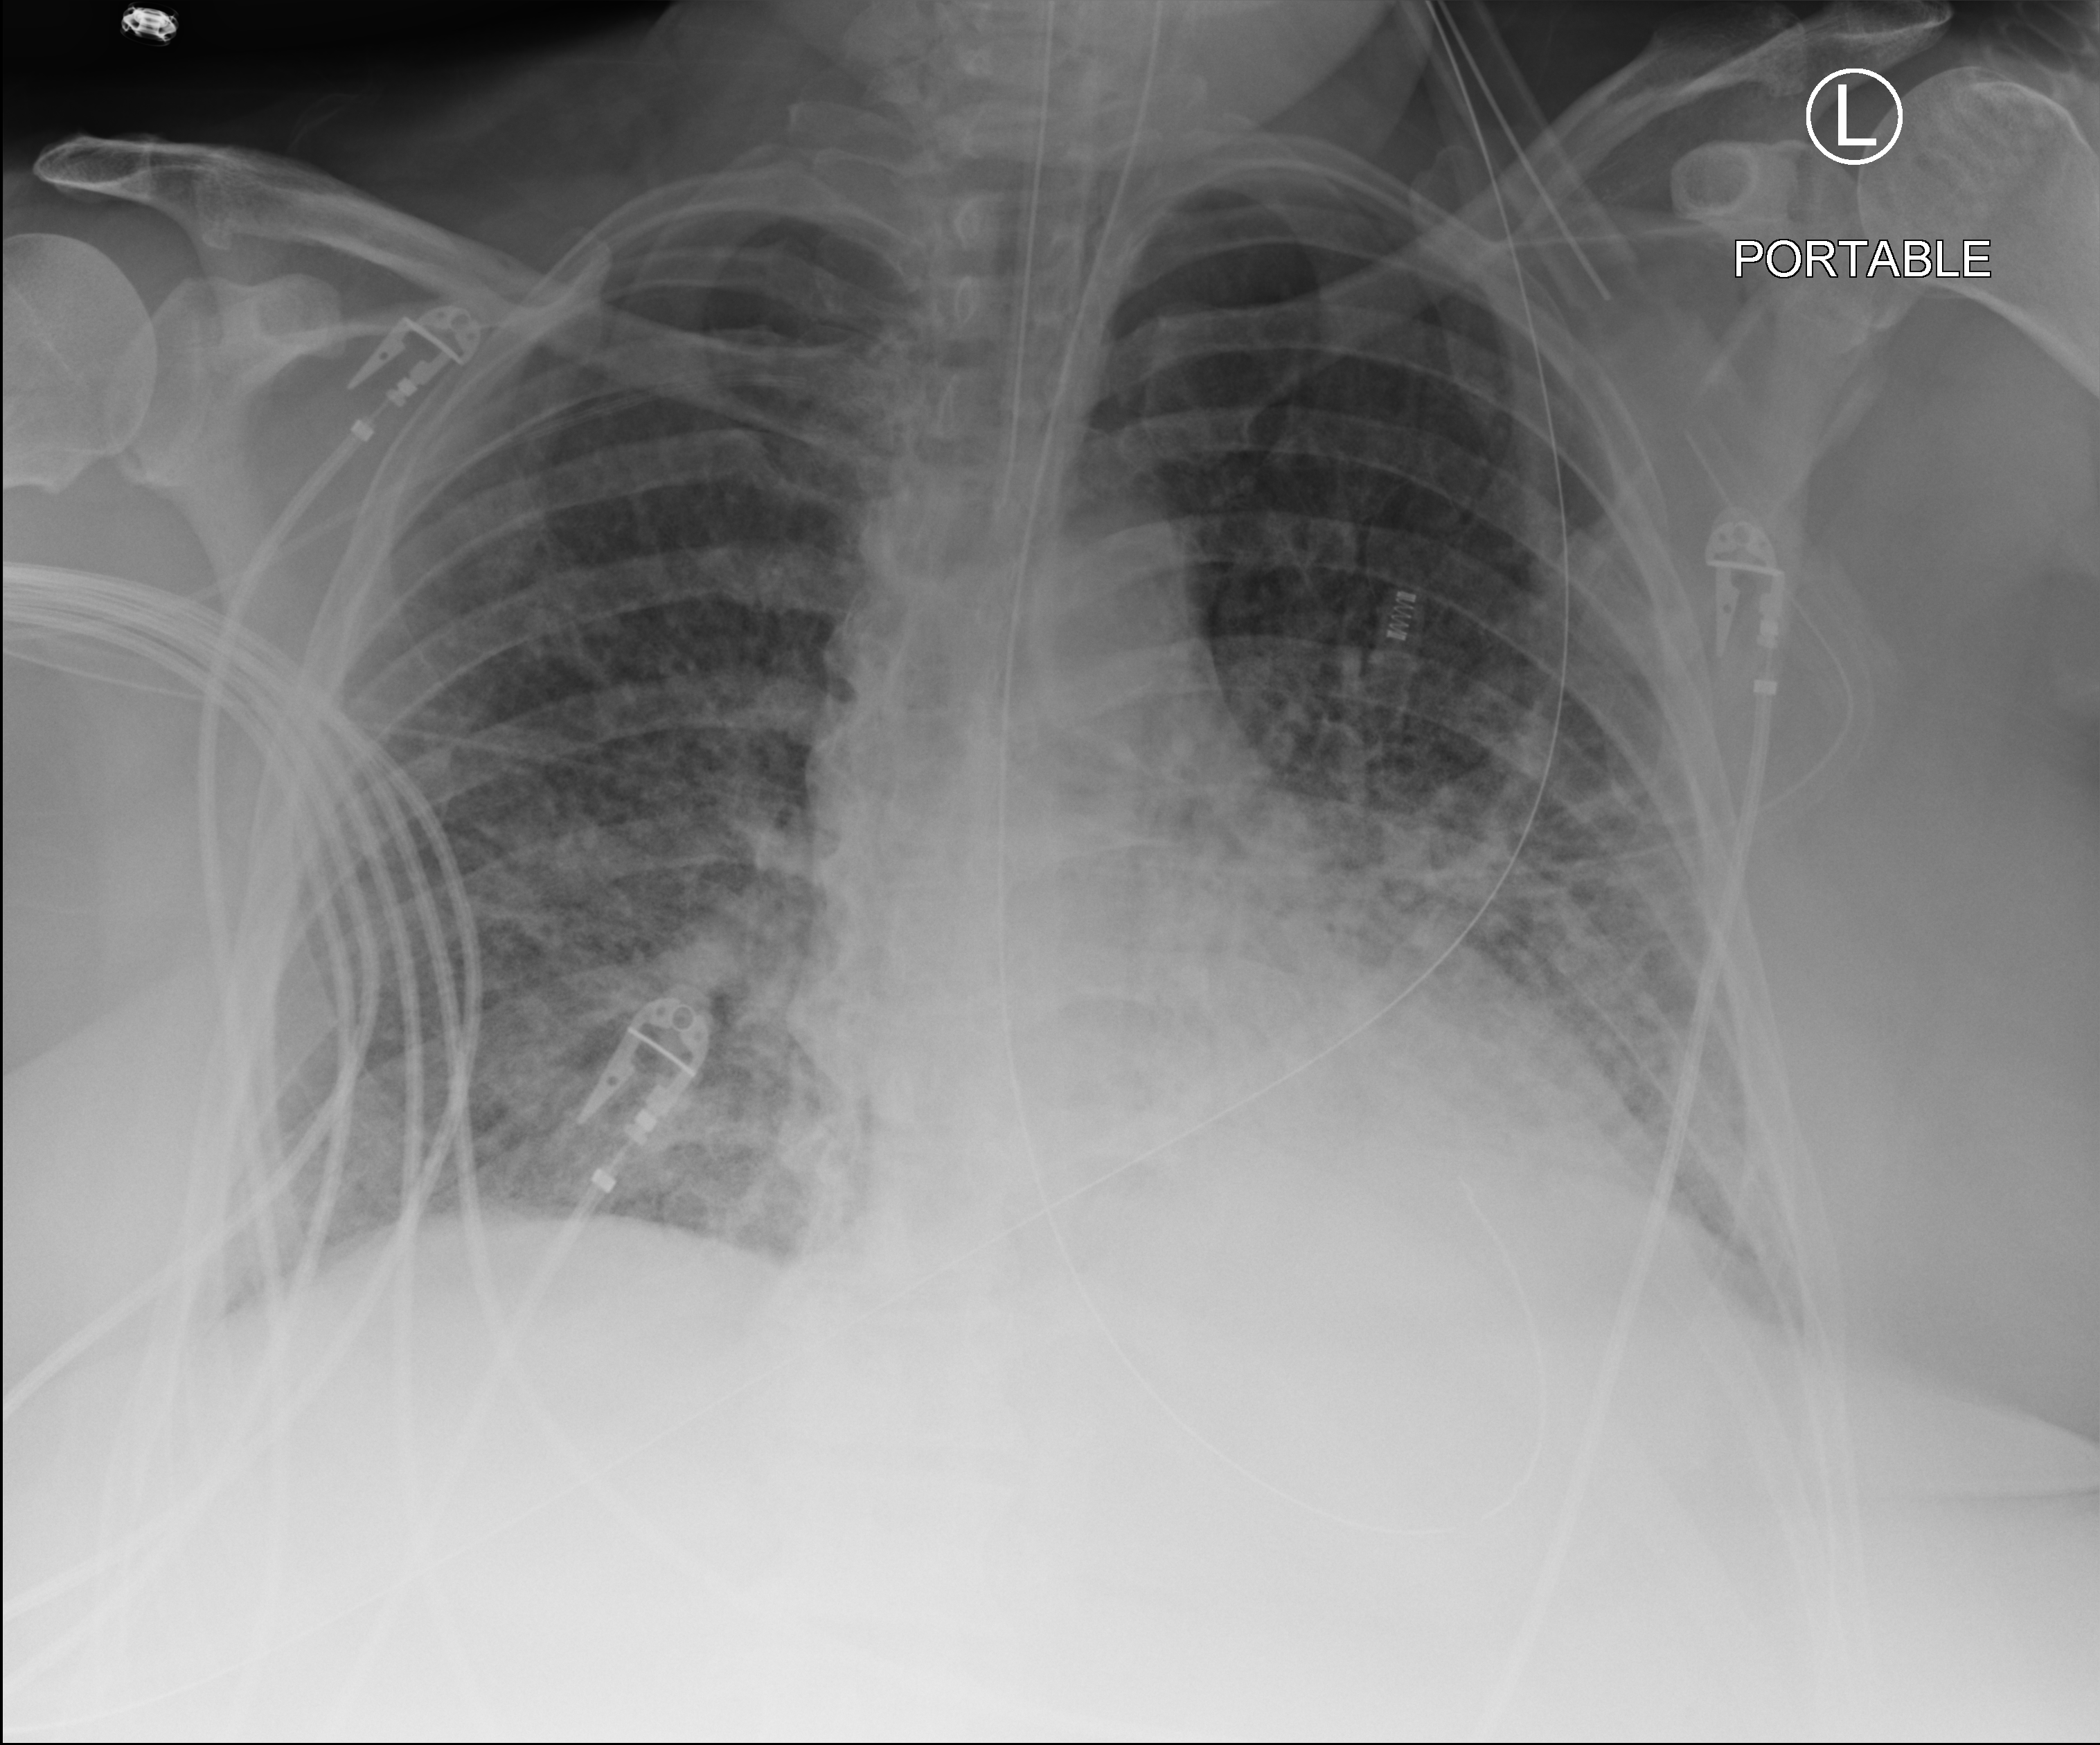
Chest X-ray (portable); anteroposterior (AP) projection. Adult patient hospitalised with COVID-19, age 18–59 years.
Hospital-stay facts (about this admission, not read from this image; timing relative to this image not recorded):
- admitted to intensive care during this hospital stay: yes
- mechanically ventilated during this hospital stay: yes